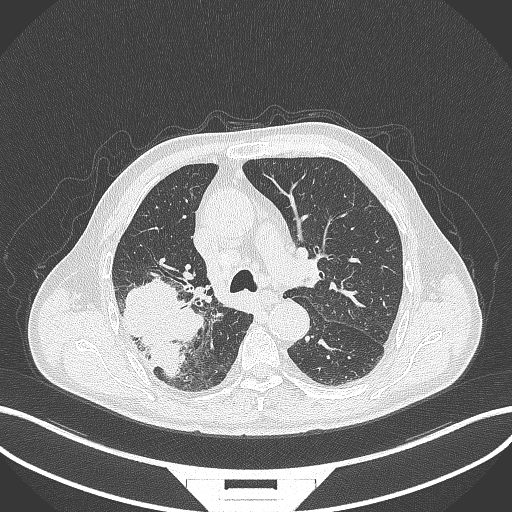
Chest CT, one axial slice. Slice 272 of 429 in the series (ordered by position). Reconstruction kernel B70f. Lung window (W 1500 / L -600 HU). 1 mm slice thickness. 512 × 512 image matrix, field of view 400 × 400 mm. Male patient, age 72 years. From the clinical record (not read from this slice): clinical TNM (as recorded): T3 N2 M0.
Structures marked on this image (bounding box drawn by a radiologist):
- lung tumour (recorded histology: adenocarcinoma): bounding box [x1, y1, x2, y2] px = [117, 269, 204, 383]